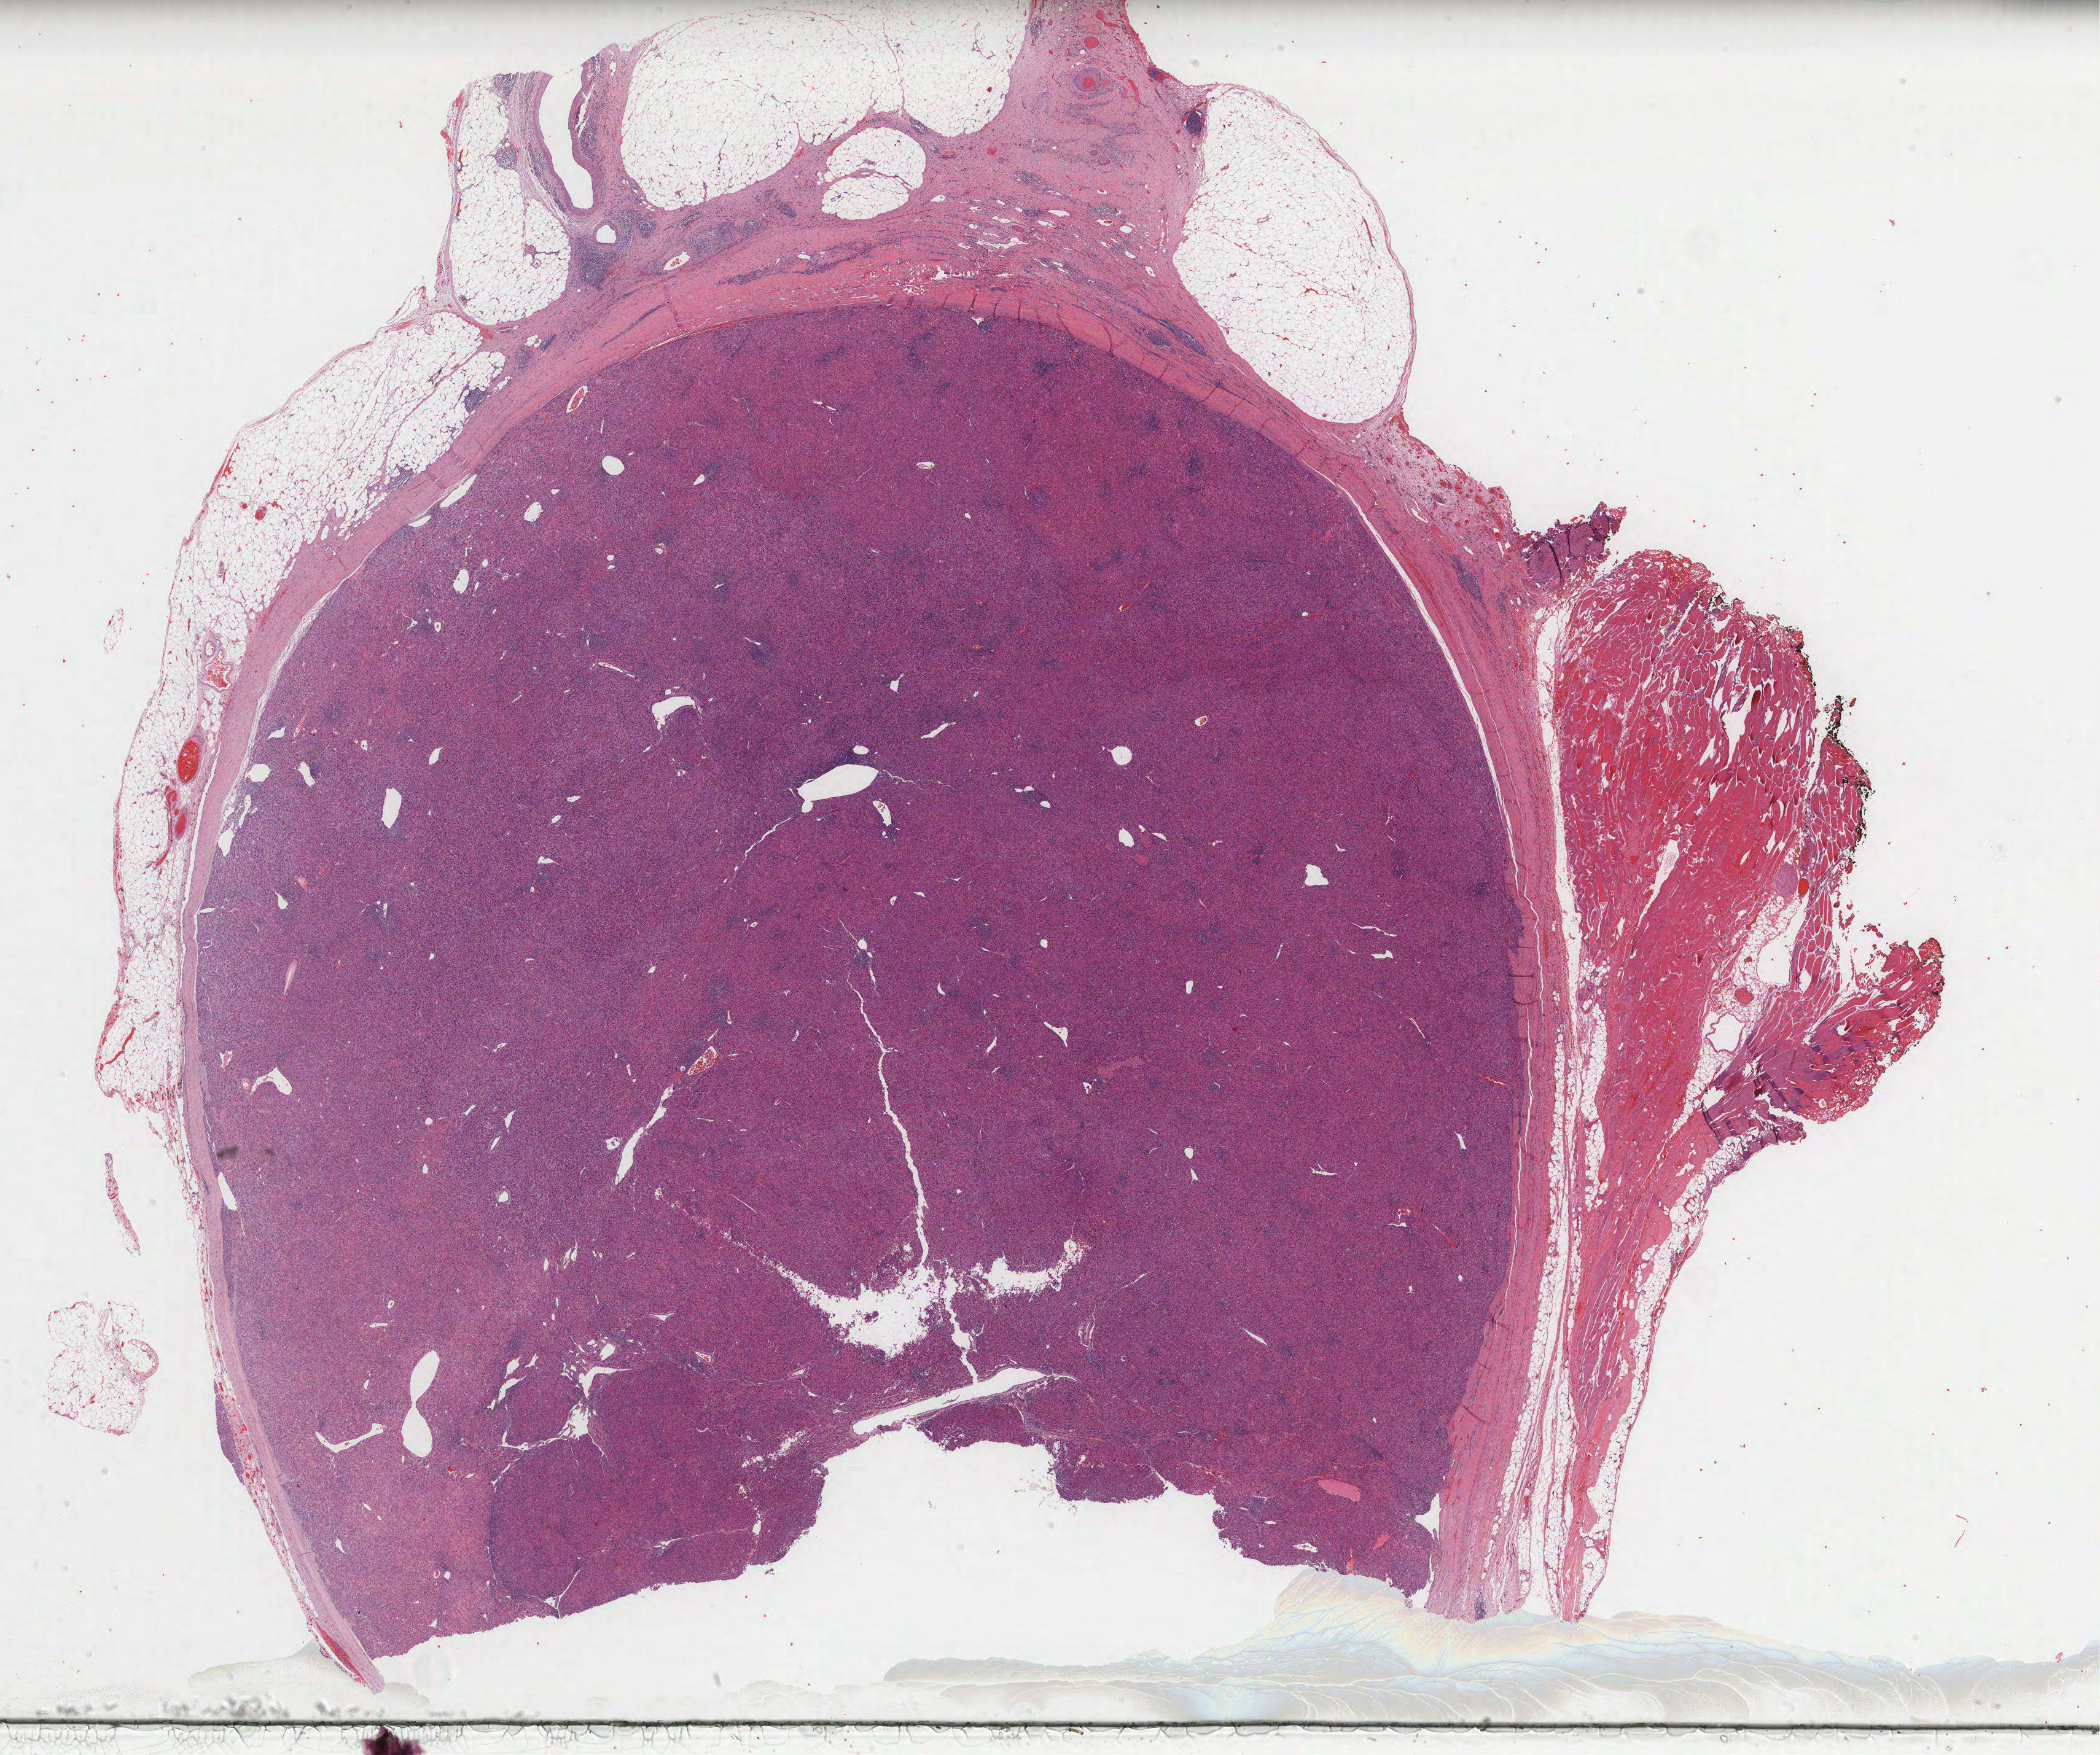
Digitized H&E-stained tissue section (whole slide) — whole scanned area (about 27.6 x 23.1 mm, slide scanned at 40x) shown as a low-resolution overview; FFPE section; sample: primary tumour, liver. Male patient; age at initial diagnosis 45 years. Histologic grade: G1 (well differentiated).
• TNM: T2 NX MX
• AJCC pathologic stage: II
• histologic diagnosis: Hepatocellular carcinoma, NOS